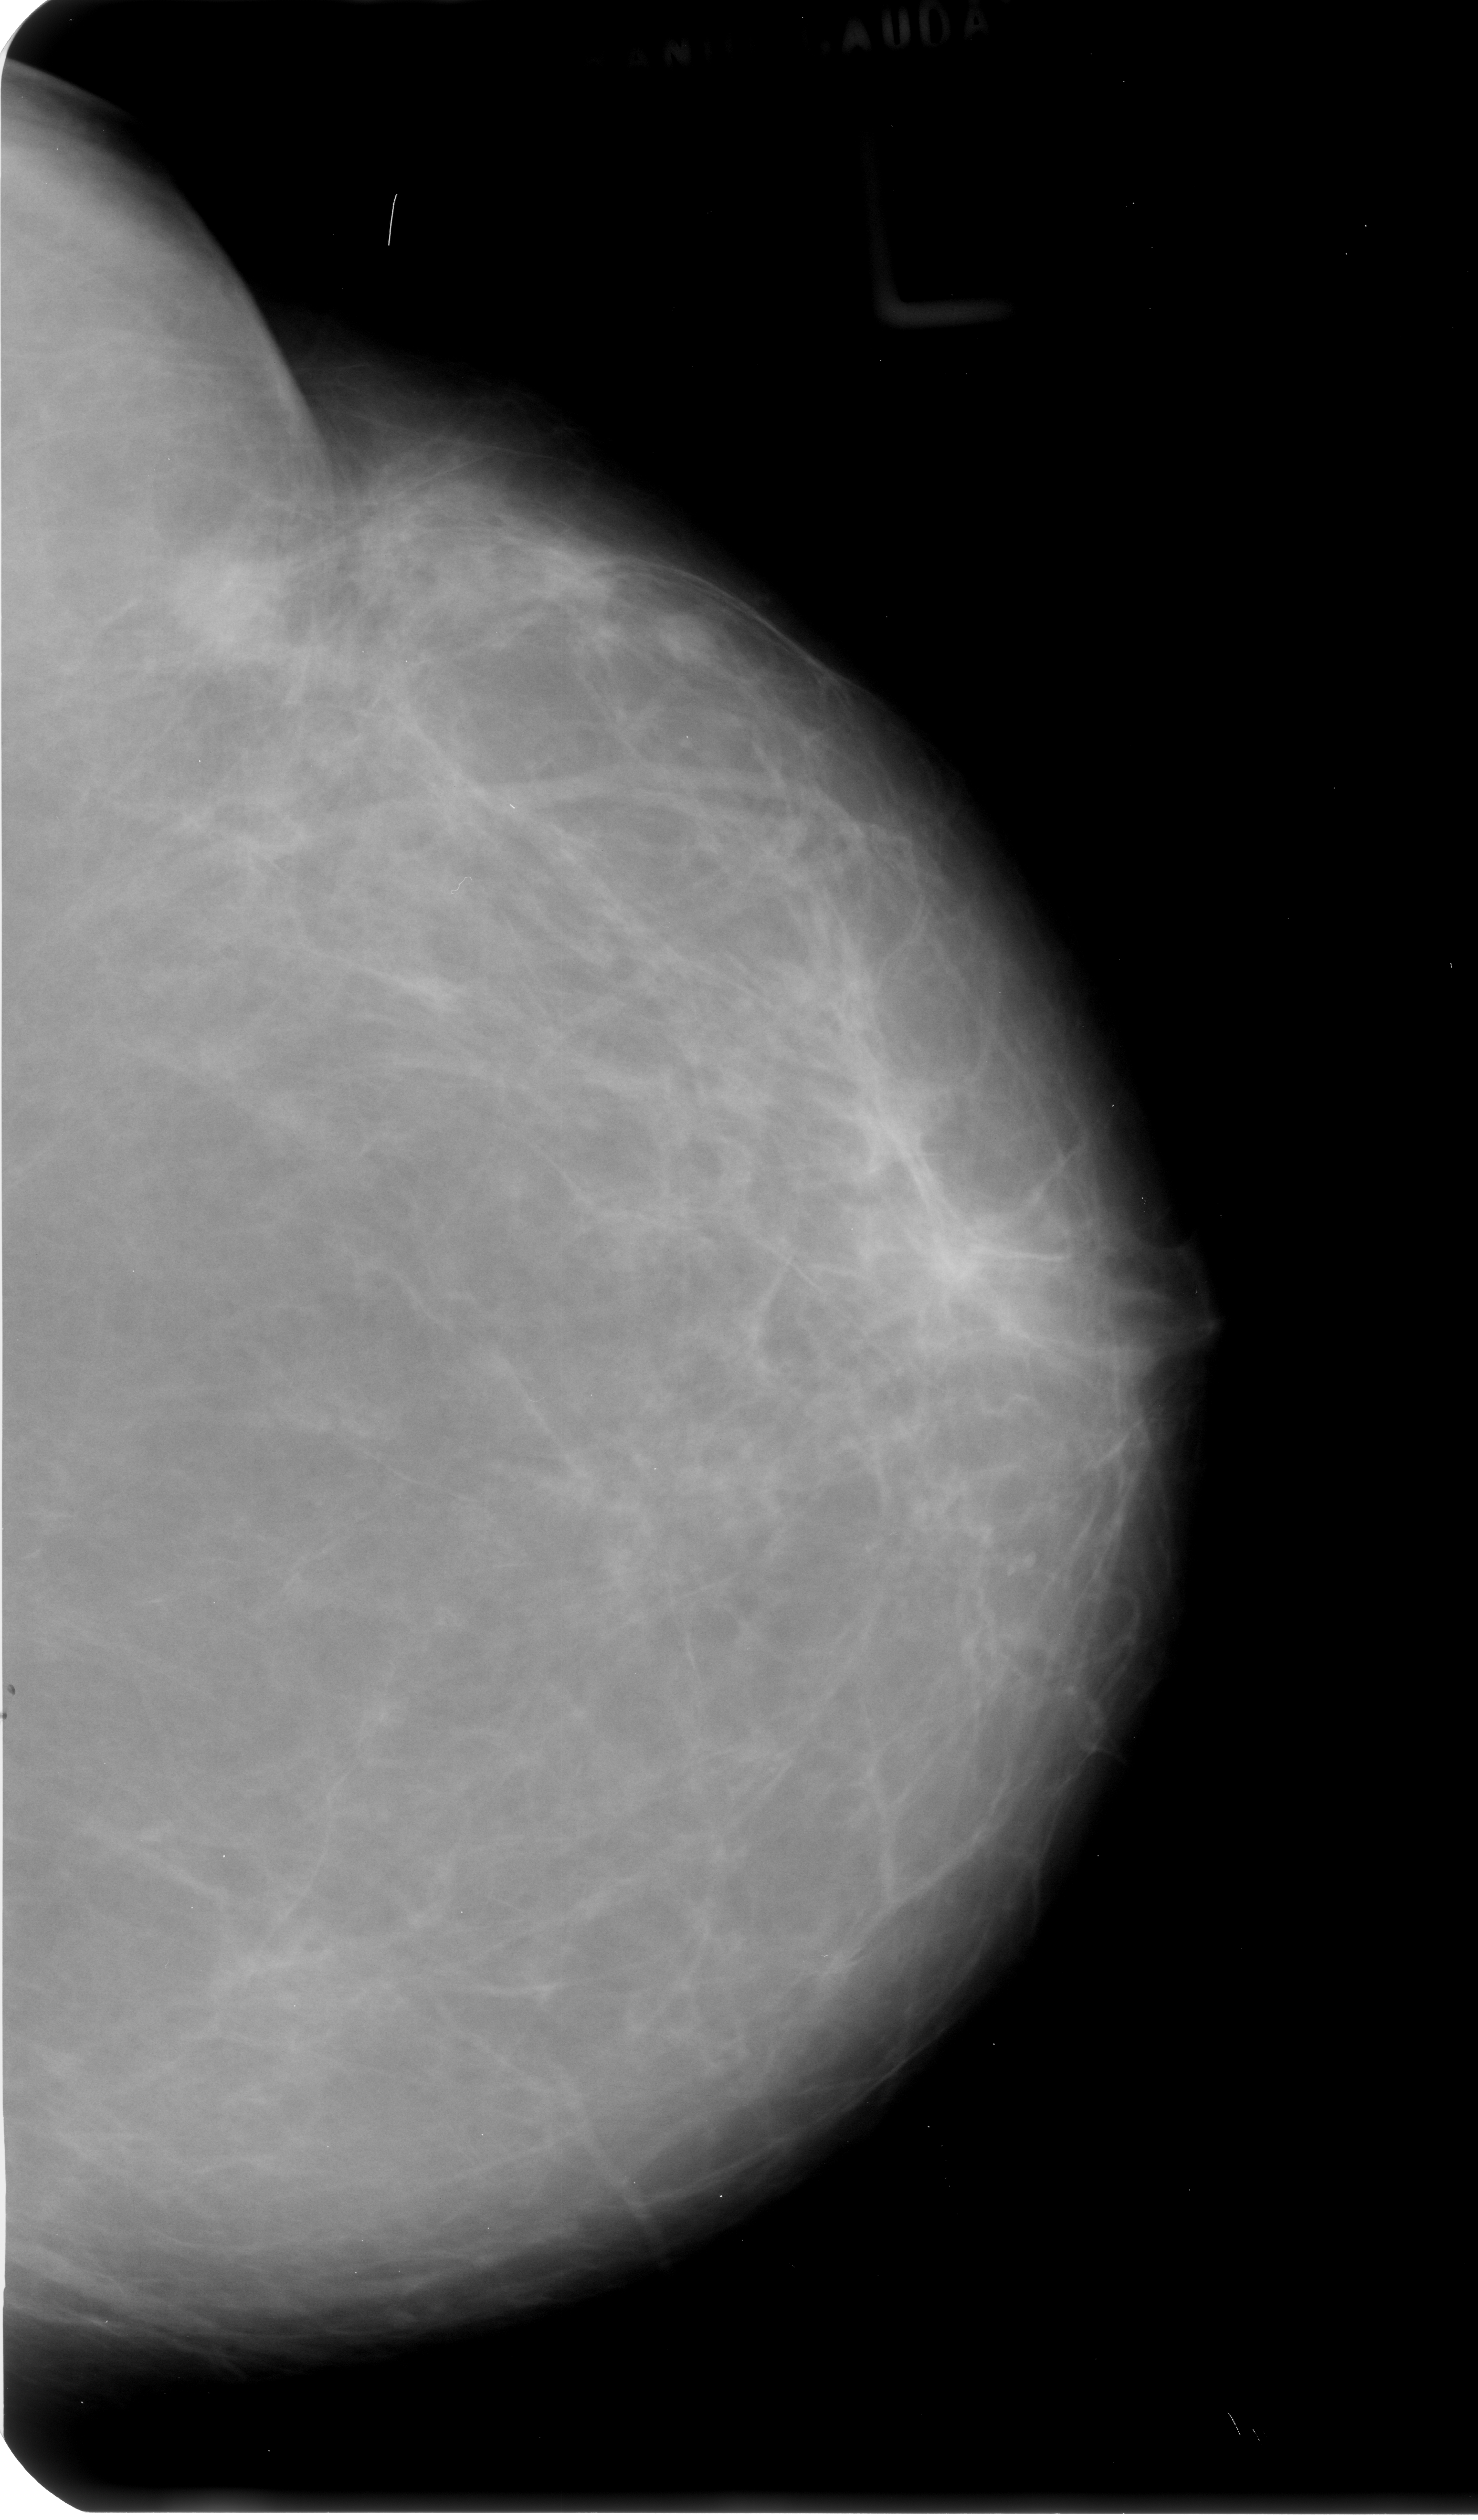
Digitized screen-film mammogram; left breast; craniocaudal (CC) view; breast composition: scattered fibroglandular densities (BI-RADS density category 2 of 4).
Marked abnormality: mass, shape irregular, margins spiculated; BI-RADS assessment category 4; subtlety rating 4 on a 1 (subtle) to 5 (obvious) scale; pathology (as recorded): malignant.